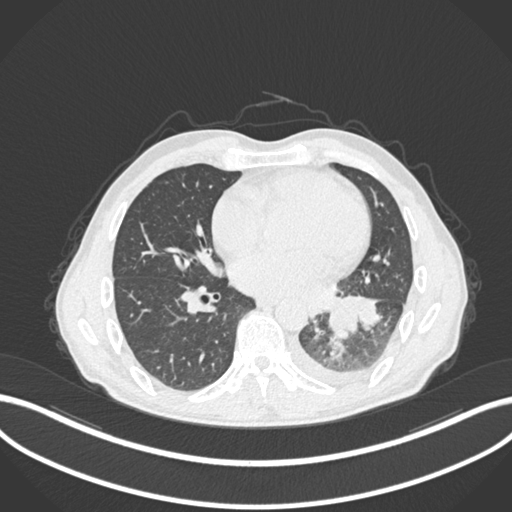
Chest CT, one axial slice; slice 103 of 222 in the series (ordered by position); 120 kVp; lung window (W 1500 / L -600 HU); 1 mm slice thickness; 512 × 512 image matrix, field of view 400 × 400 mm. Patient: male, 47 years. Case-level facts recorded for this patient, not image findings: clinical TNM (as recorded): T3 N1 M1c; histopathological grade: G3.
Structures marked on this image (bounding box drawn by a radiologist):
- lung tumour (recorded histology: small cell carcinoma): bounding box <328,294,361,340> (left, top, right, bottom; pixels)